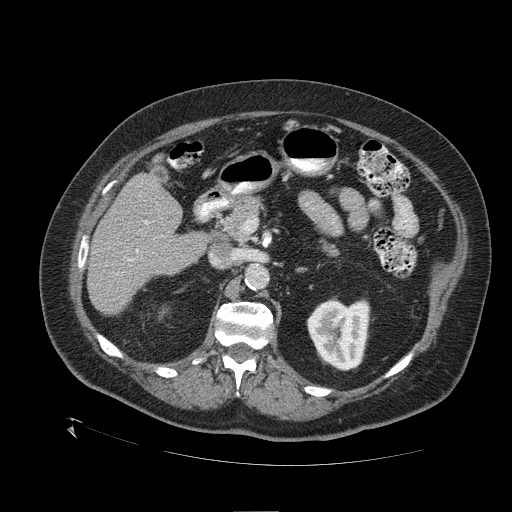
Contrast-enhanced abdominal CT (liver protocol), one axial slice; slice 58 of 109 in the series (ordered by position); reconstruction kernel STANDARD; one of 2 acquisitions stored at this slice position; soft-tissue window (W 400 / L 40 HU); 2.5 mm slice thickness; 512 × 512 image matrix, field of view 460 × 460 mm. Case-level facts recorded for this patient, not image findings: diagnosis: hepatocellular carcinoma (patient treated with transarterial chemoembolisation; whether this scan precedes or follows treatment is not stated here); TNM stage (as recorded): Stage-I.
Annotated regions visible in this slice (semi-automatically segmented with operator editing):
- liver parenchyma outside the tumour (the mass and vessels are separate outlines, so this box may not span the whole liver): bounding box [x1, y1, x2, y2] px = [88, 174, 206, 314]
- liver vessels: [128, 221, 149, 261]